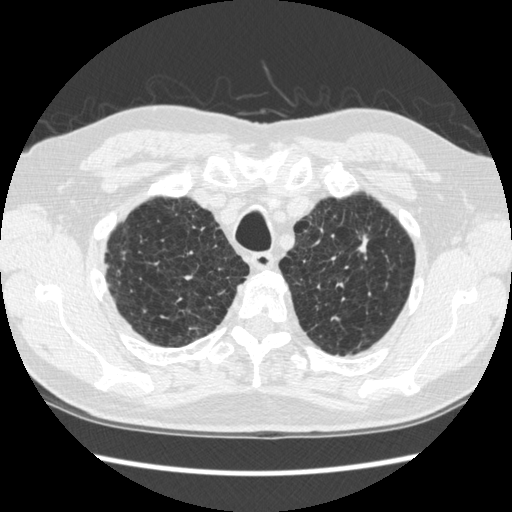
Chest CT (low-dose screening protocol), one axial image. Second annual screen. Lung window (W 1500 / L -600 HU). 1.25 mm slice thickness. Standard (soft-tissue) reconstruction kernel (STANDARD). Slice 48 of 295 in the series. Male participant, aged 70 years at enrolment. Former smoker at enrolment.
Lesion marked by an expert reader, bounding box <332,217,393,284> (left, top, right, bottom; pixels). The screening reader recorded 5 non-calcified nodules or masses ≥4 mm on this exam (right lower lobe, right lower lobe, right lower lobe, left upper lobe, left lower lobe); which of them this box marks is not recorded. Official screen result: positive, change unspecified: nodule(s) >= 4 mm or enlarging nodule(s), mass(es), or other non-specific abnormalities suspicious for lung cancer. Participant outcome: lung cancer diagnosed 479 days after this screen (after the third annual screen) — squamous cell carcinoma, NOS, left upper lobe, moderately differentiated (G2), stage IA (AJCC 6th edition), 18 mm at pathology.